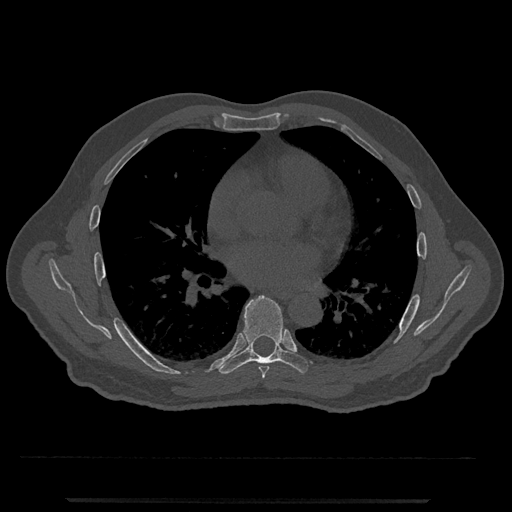
CT including the spine, one axial slice; slice 699 of 797 in the series (ordered by position); 120 kVp; bone window (W 1800 / L 400 HU); 0.5 mm slice thickness; 512 × 512 image matrix, field of view 419 × 419 mm. Patient: male, 63 years. Case-level facts recorded for this patient, not image findings: primary cancer: prostate.
Structures marked on this image (semi-automatic segmentation, software-assisted and operator-edited):
- T6 vertebra: bounding box <259,366,270,379> (left, top, right, bottom; pixels)
- T7 vertebra: <217,296,308,374>